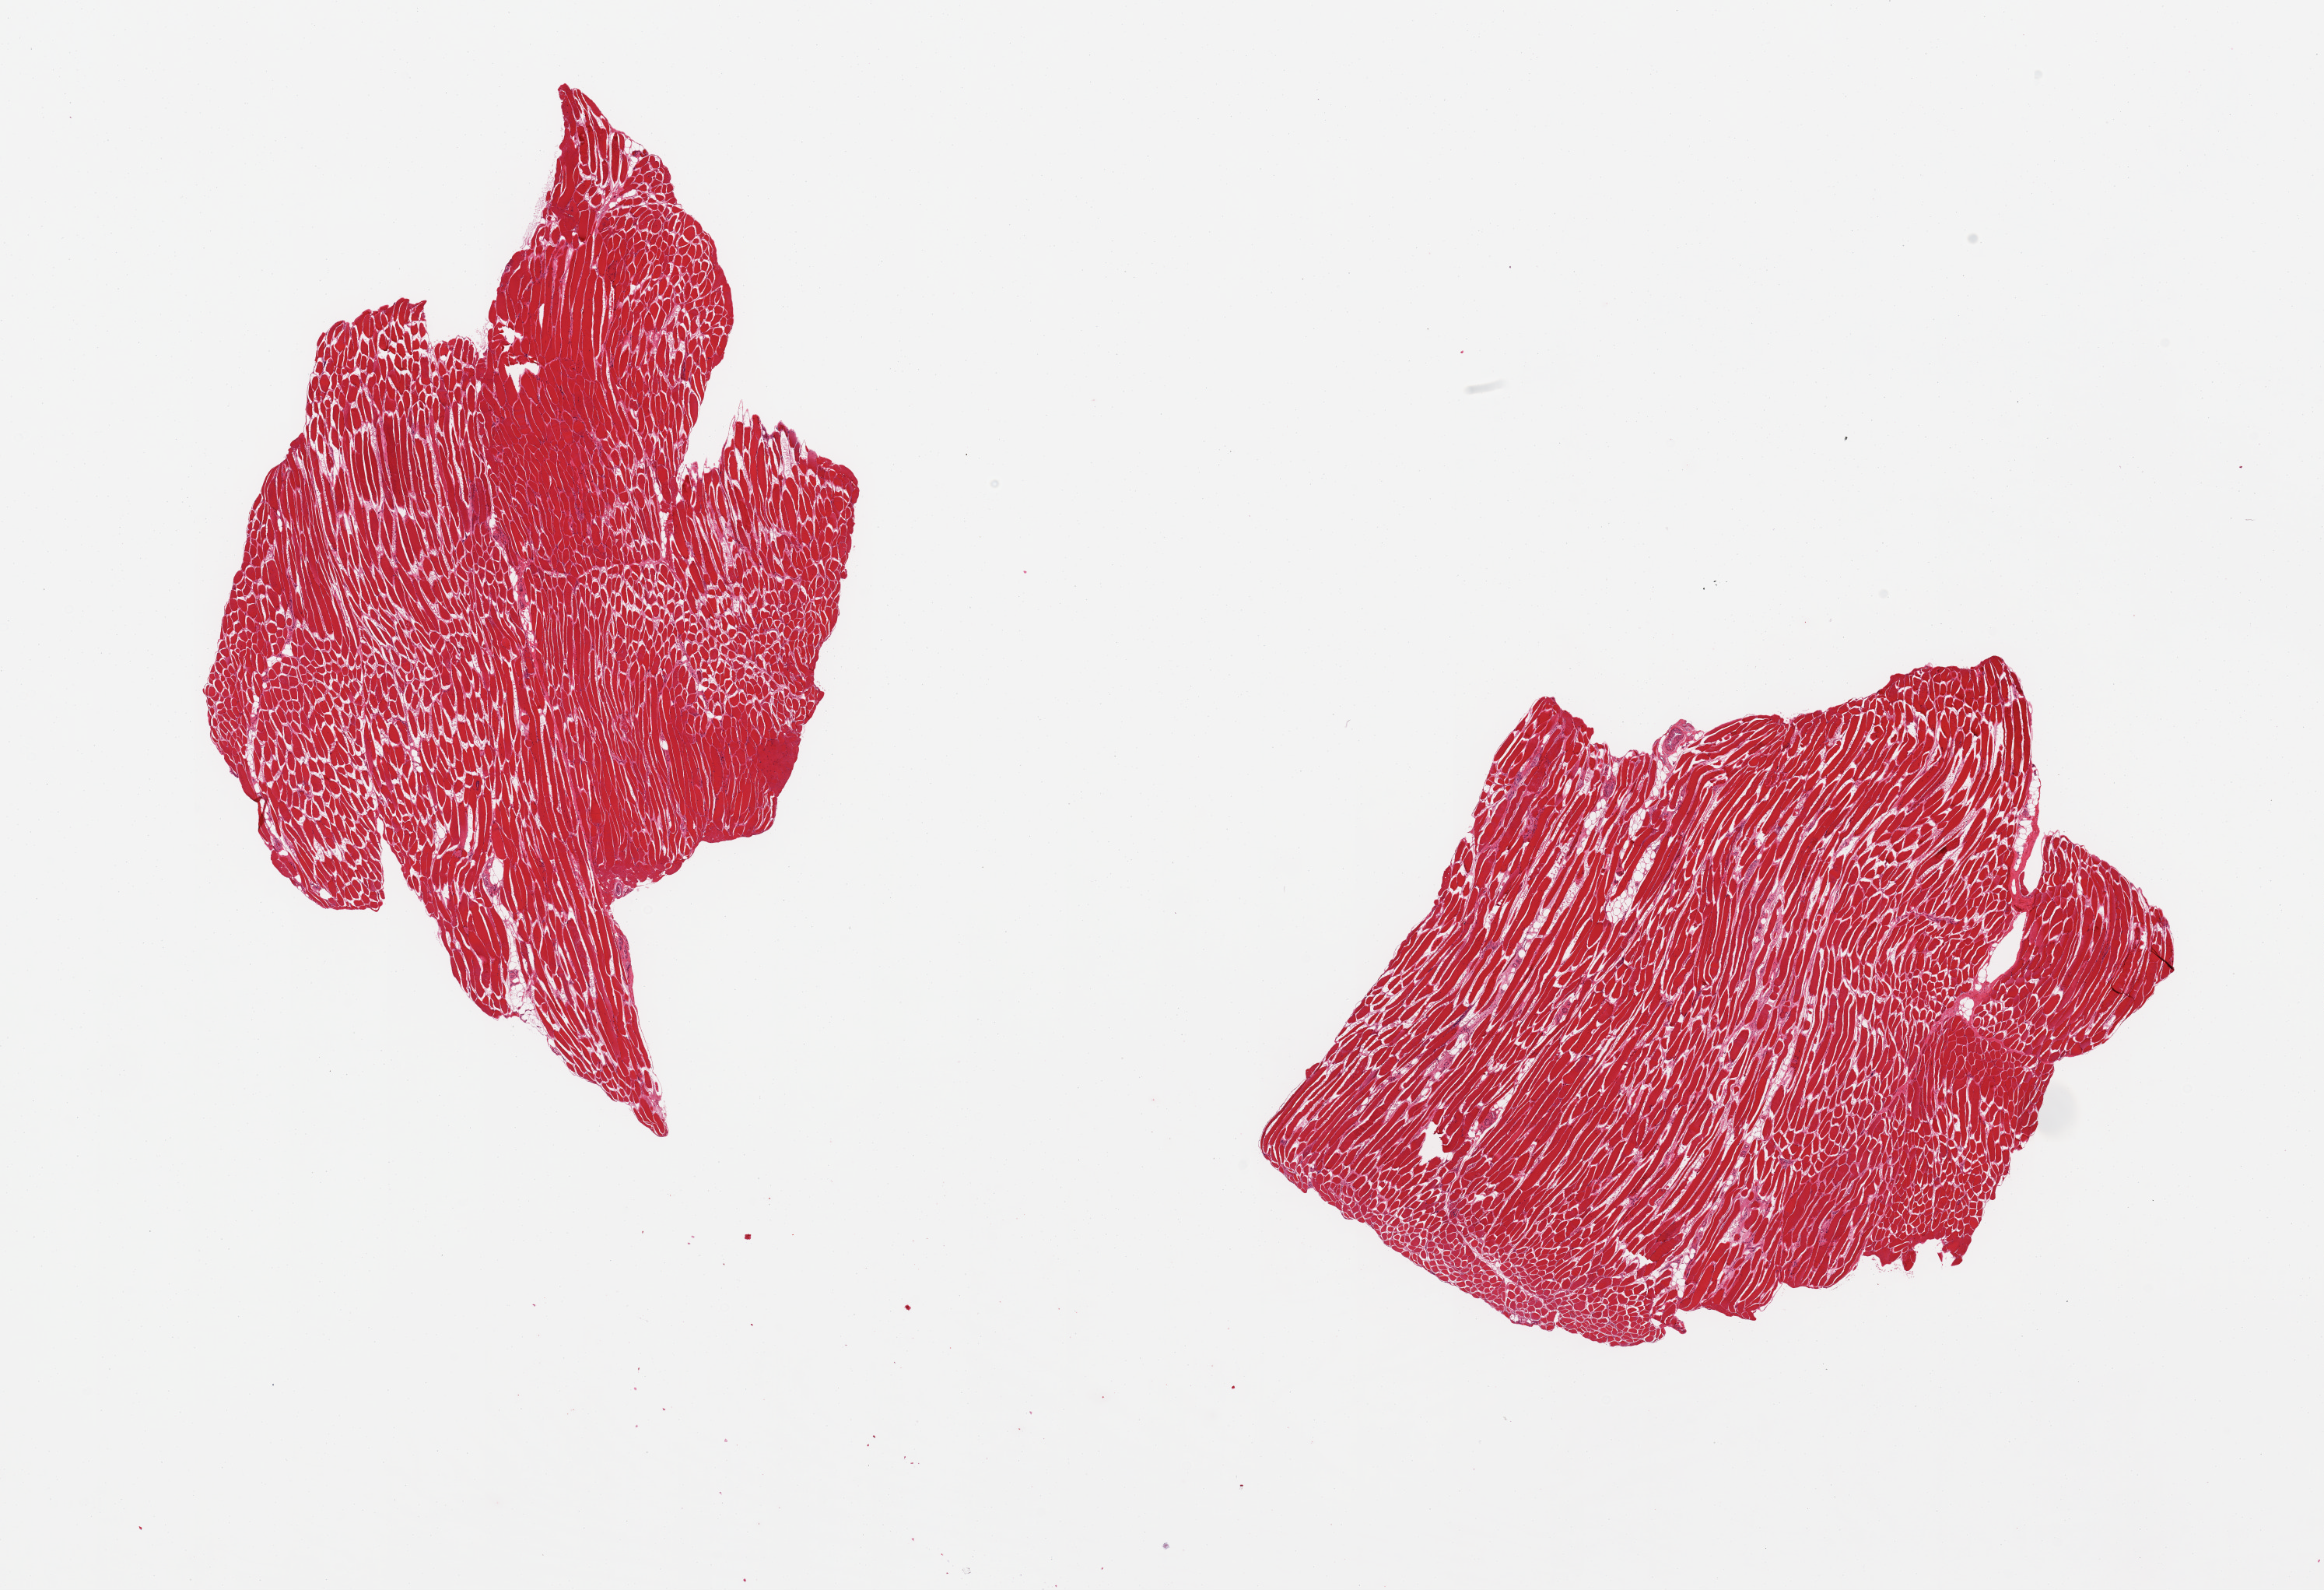
Hematoxylin and eosin (H&E) whole-slide image, brightfield, whole scanned area (about 23.6 x 16.2 mm, acquisition: 20x scan) shown as a low-resolution overview; PAXgene-fixed, paraffin-embedded tissue; sampled site (target tissue): skeletal muscle; donor tissue sample. Donor sex: male.
Pathologist's review note for this sample: 2 pieces, minimal interestitial fat.